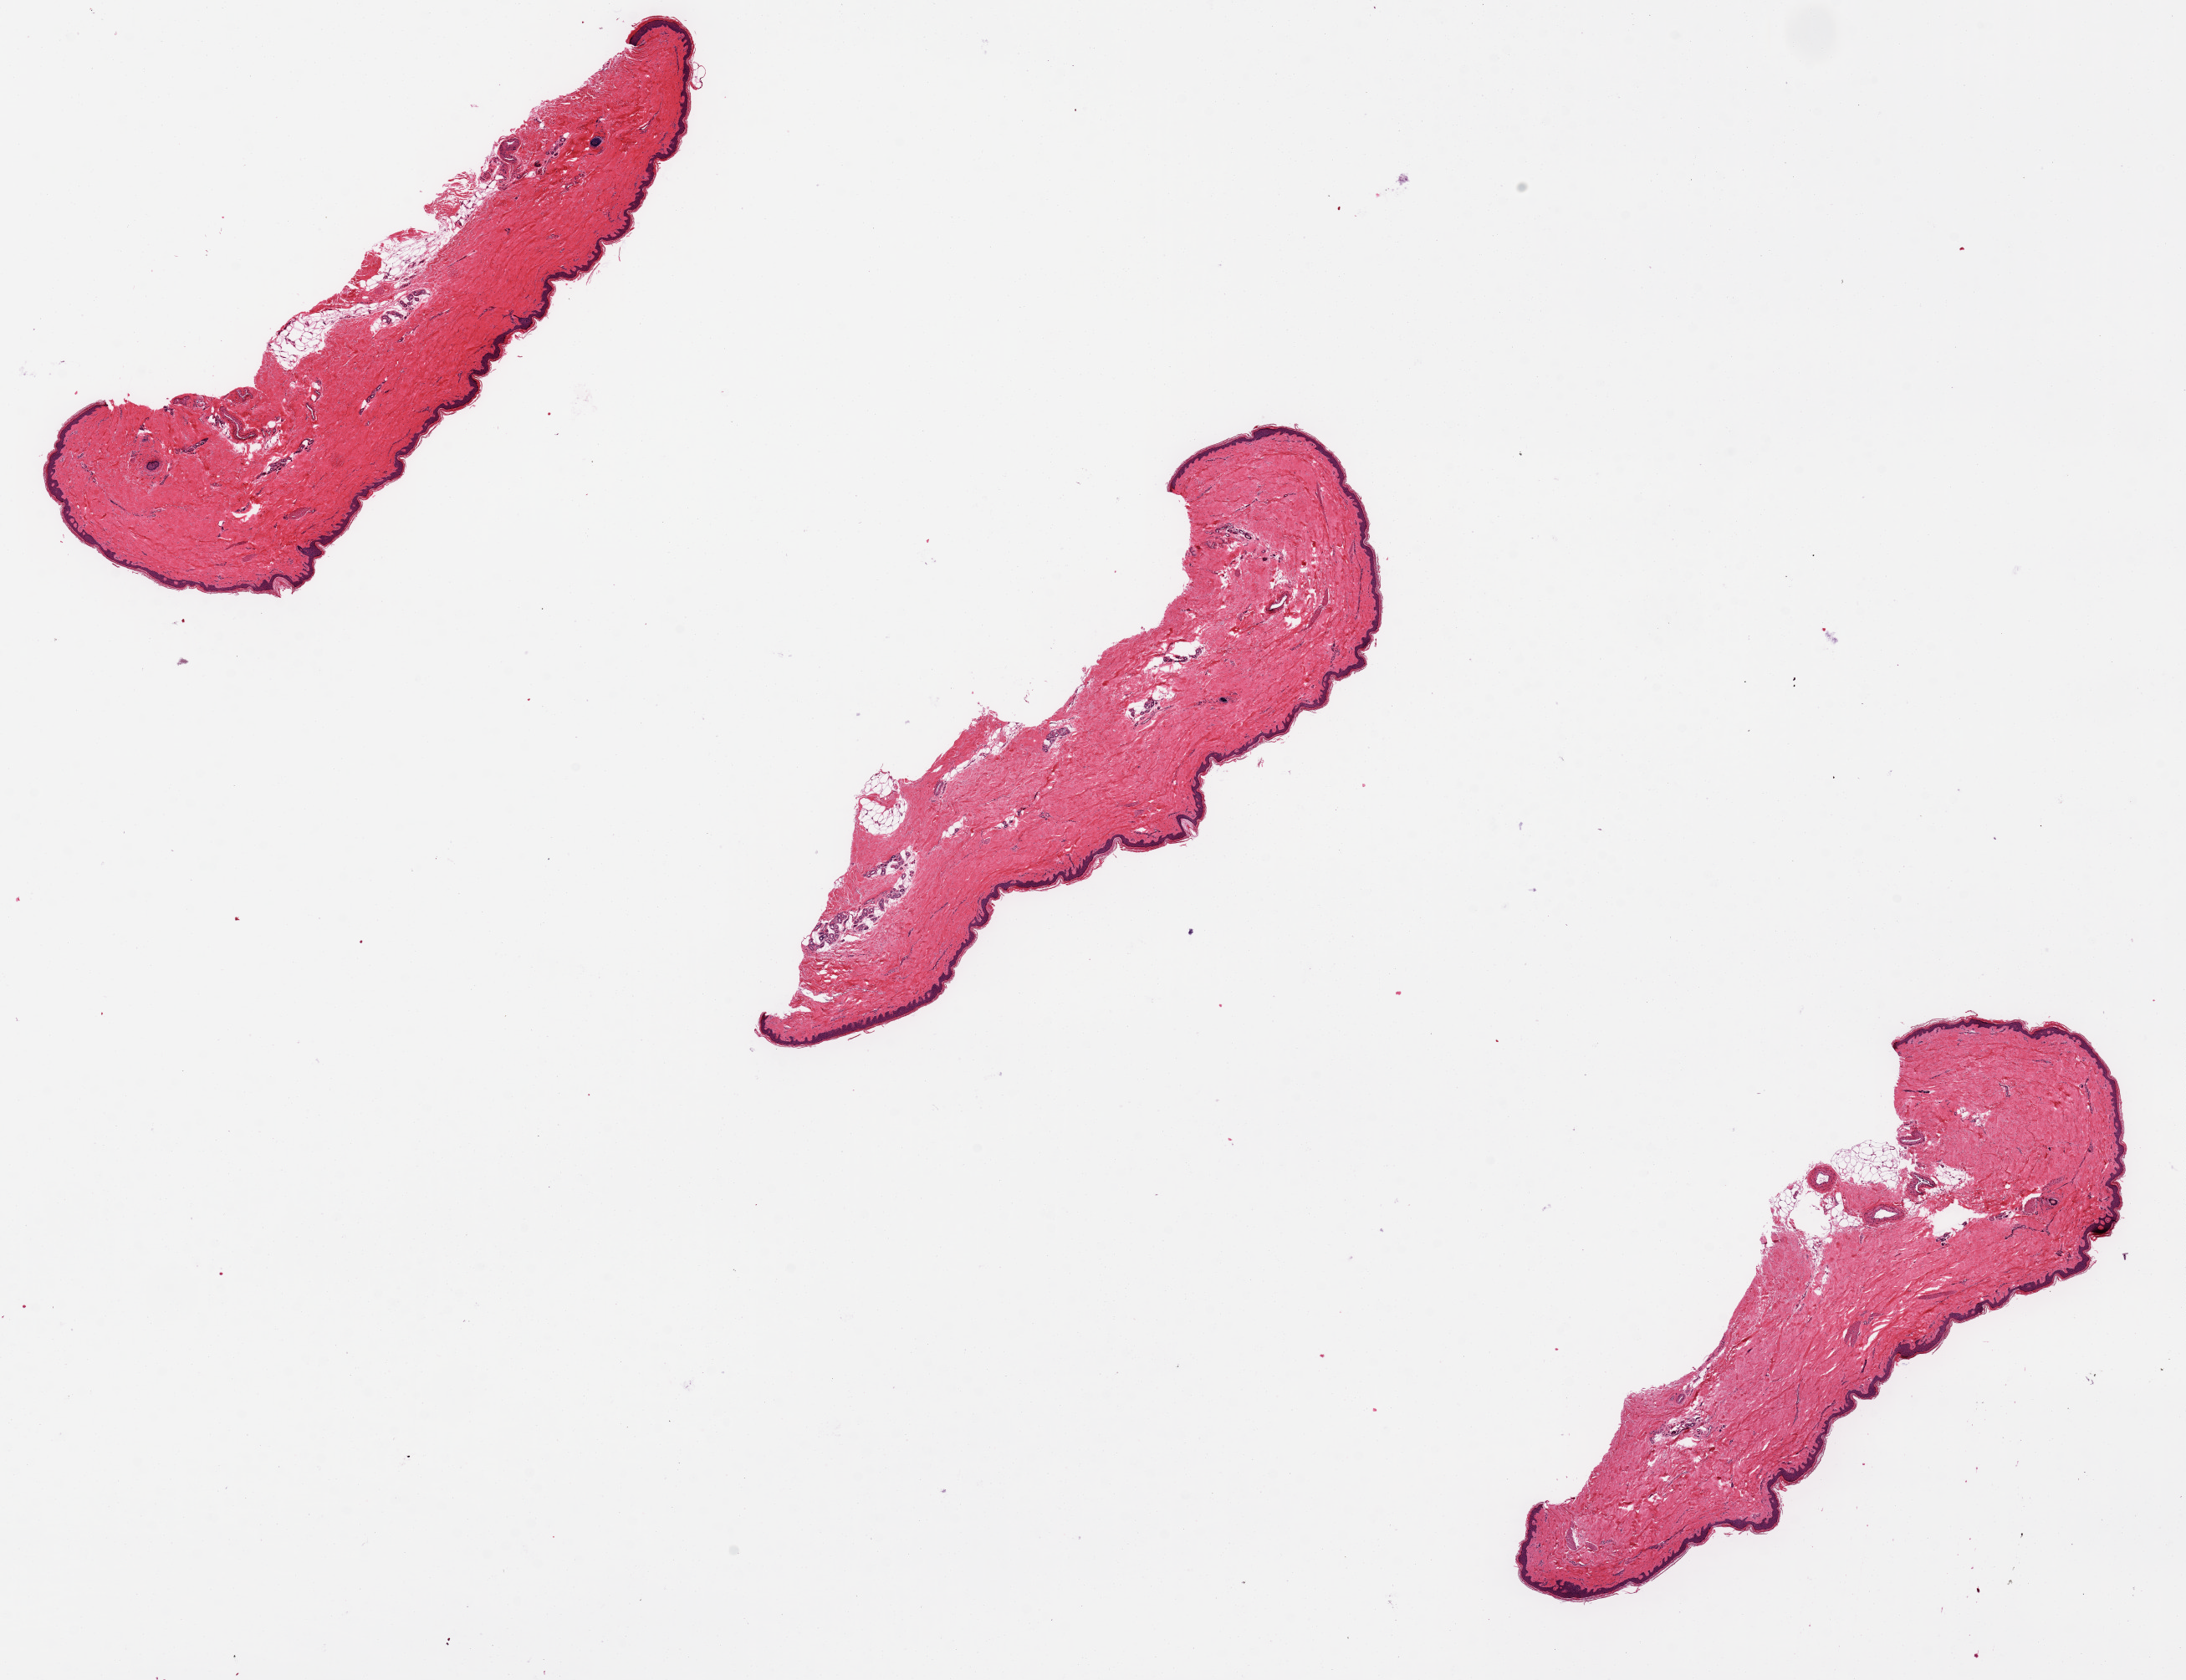
H&E whole-slide image, brightfield, a low-resolution overview of the entire scanned area, about 20.7 x 15.9 mm; PAXgene-fixed paraffin-embedded (PFPE) section; section of skin of lower leg (target tissue); donor tissue sample. Donor: female.
• reviewer comment on this tissue sample: 3 pieces